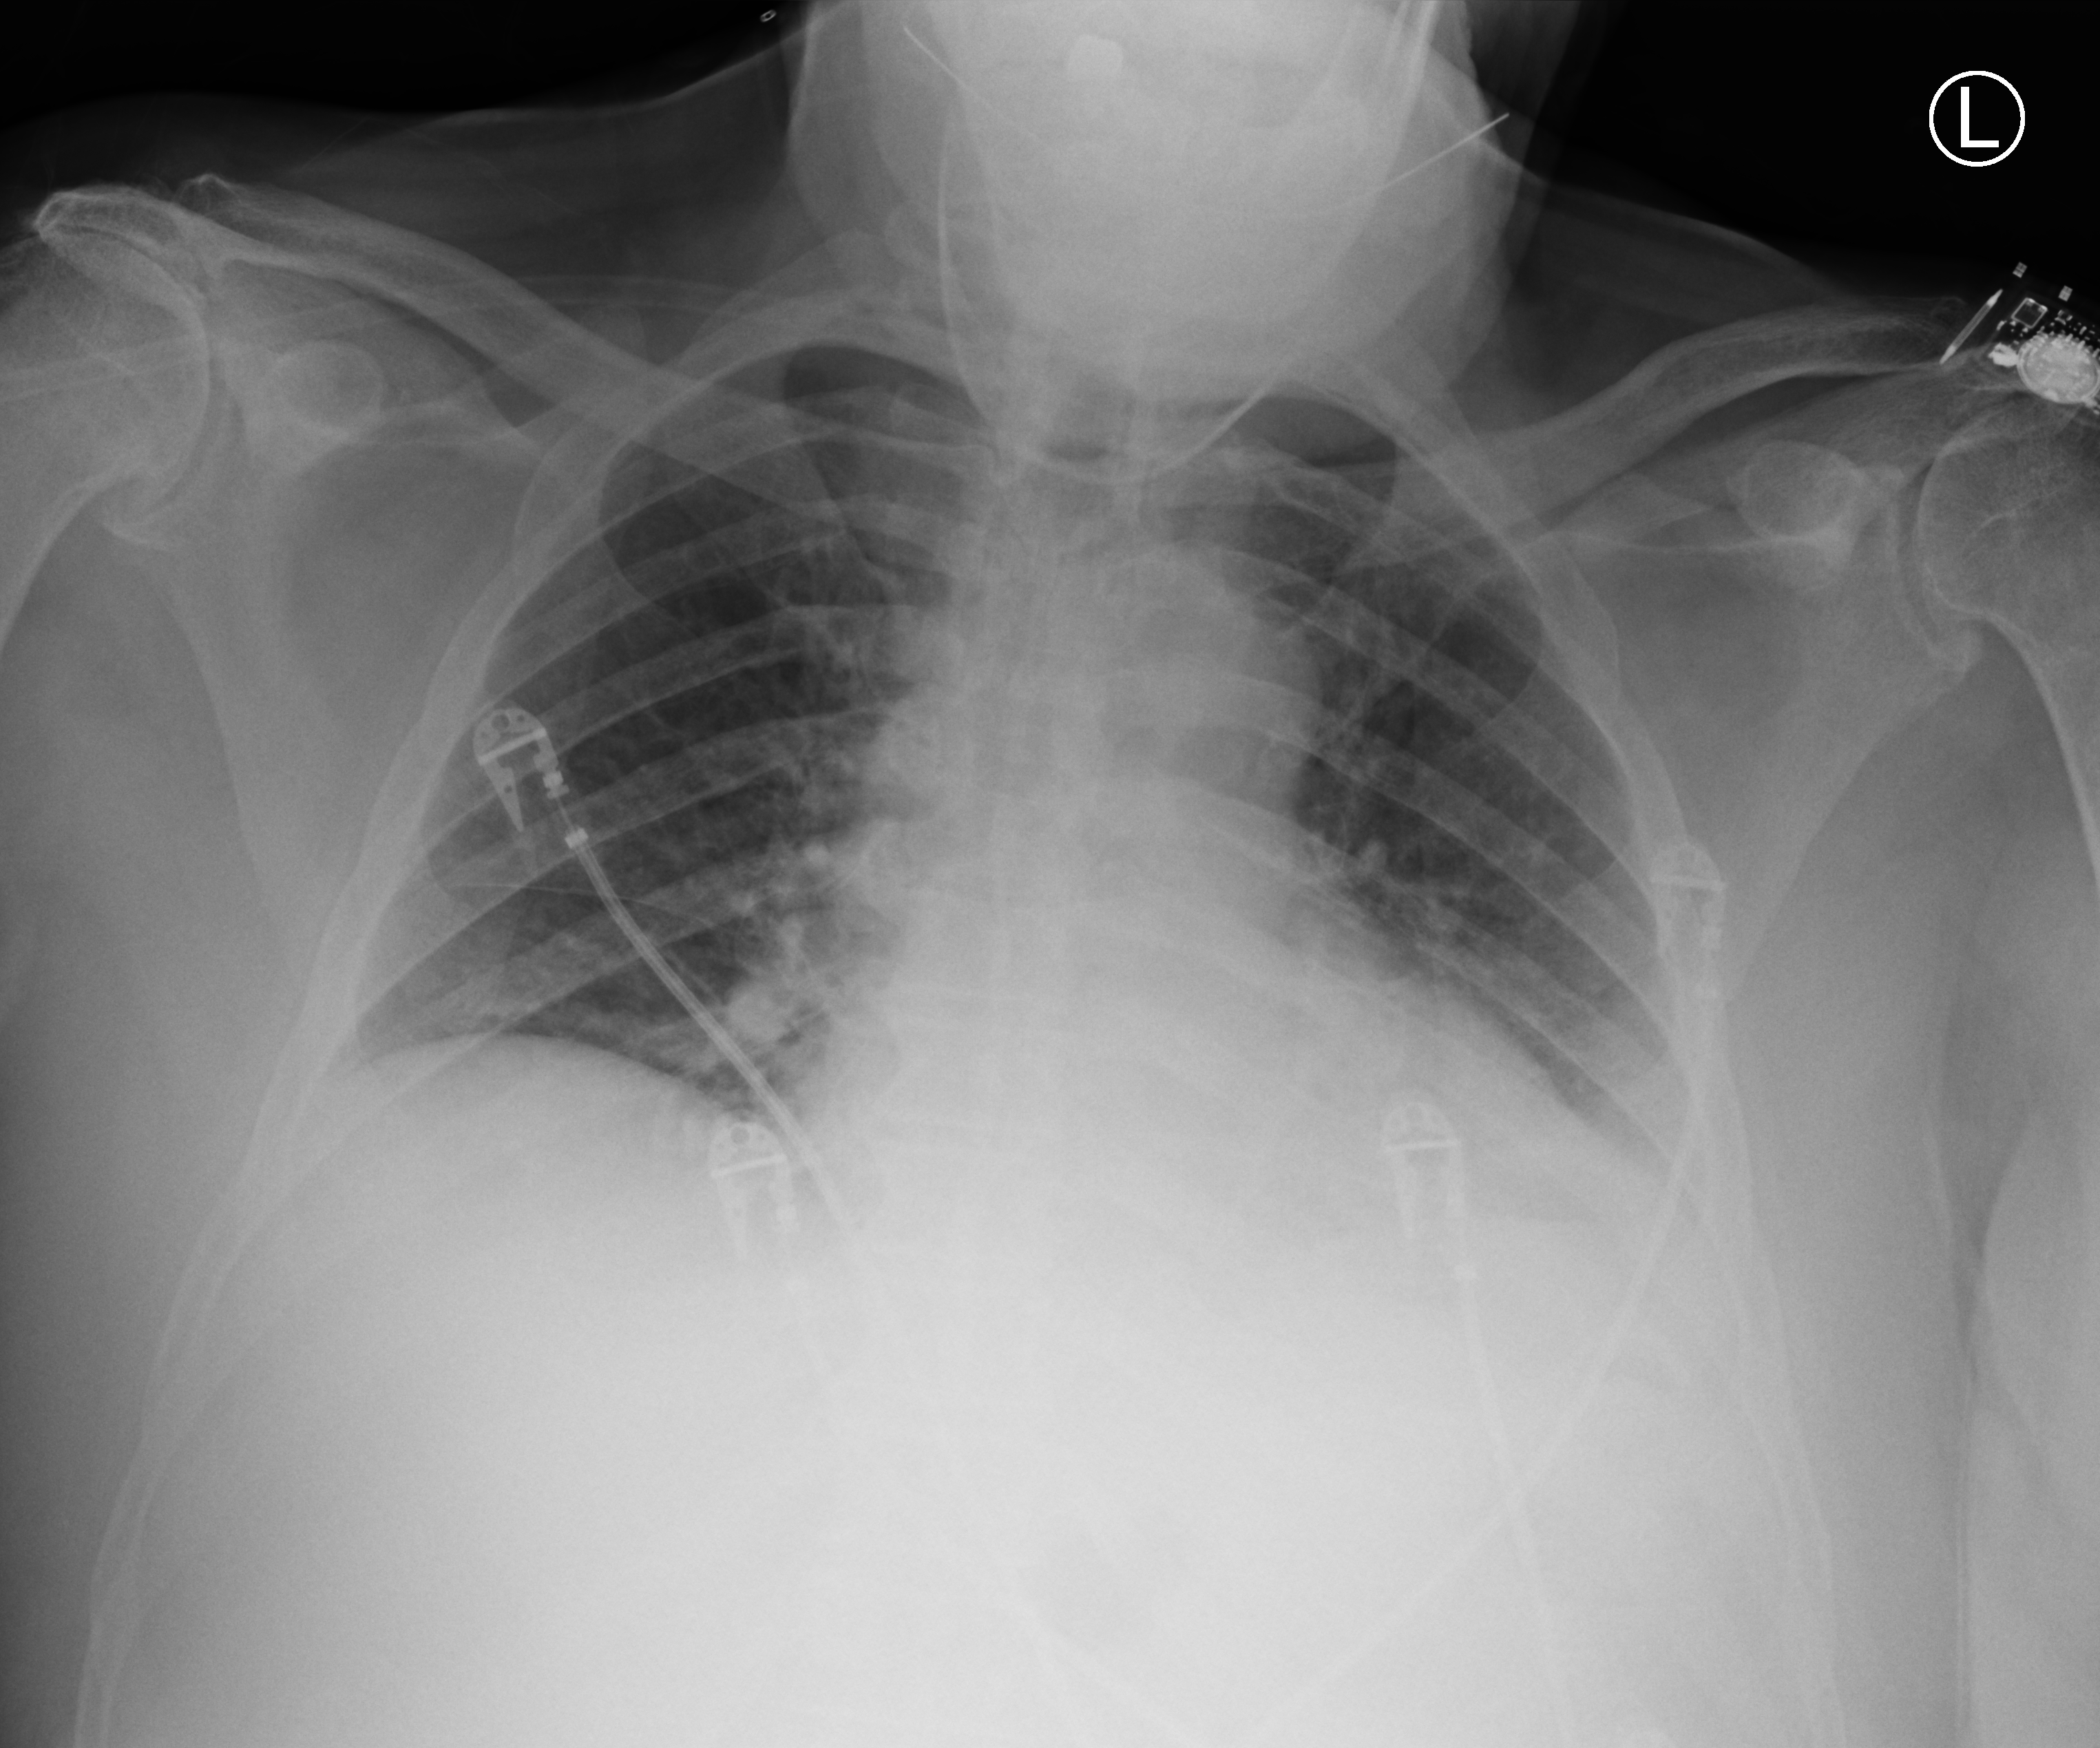
Bedside chest radiograph (computed radiography), anteroposterior (AP) projection. Patient hospitalised with COVID-19; male, aged 75–90 years.
Admission-level facts for this patient (not findings on this image; timing relative to this image not recorded):
- mechanically ventilated during this hospital stay: yes